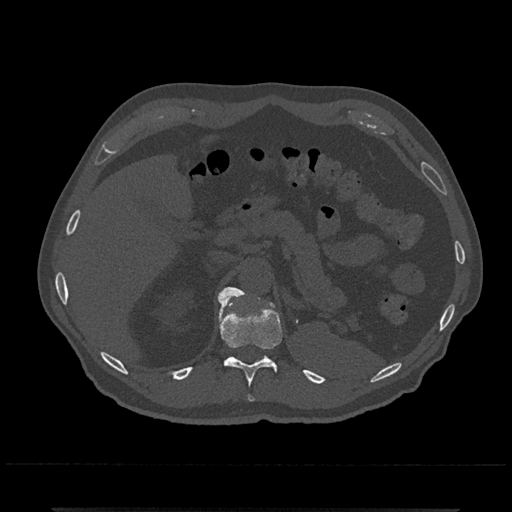
CT including the spine, one axial slice; bone window (W 1800 / L 400 HU); 0.5 mm slice thickness; 512 × 512 image matrix. Male patient, age 67 years. From the clinical record (not read from this slice): primary cancer: prostate.
Structures marked on this image (semi-automatic segmentation, software-assisted and operator-edited):
- T11 vertebra: bounding box <218,294,282,402> (left, top, right, bottom; pixels)
- T12 vertebra: <220,287,247,306>